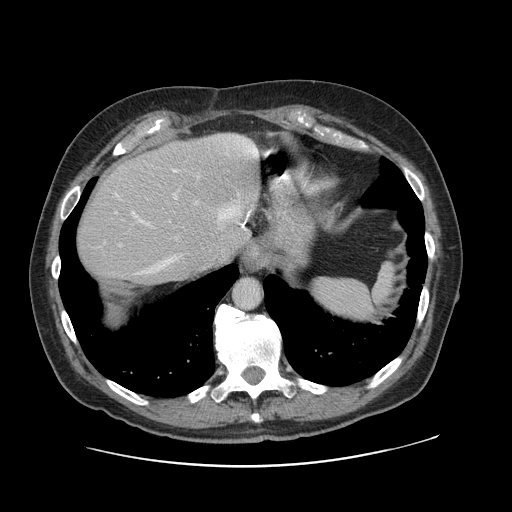
Contrast-enhanced abdominal CT, one axial slice. Slice 96 of 138 in the series (ordered by position). 120 kVp. Intravenous contrast given. Soft-tissue window (W 400 / L 40 HU). 512 × 512 image matrix, field of view 402 × 402 mm. Male patient, age 71 years. Case-level facts recorded for this patient, not image findings: diagnosis: colorectal cancer liver metastases, imaged before liver resection; multiple liver metastases: no; largest metastasis: 3.3 cm.
Structures marked on this image (expert manual segmentation):
- hepatic veins: bounding box [x1, y1, x2, y2] px = [139, 177, 250, 273]
- liver: [76, 134, 260, 287]
- planned liver remnant (the part of the liver to remain after resection): [76, 158, 226, 287]